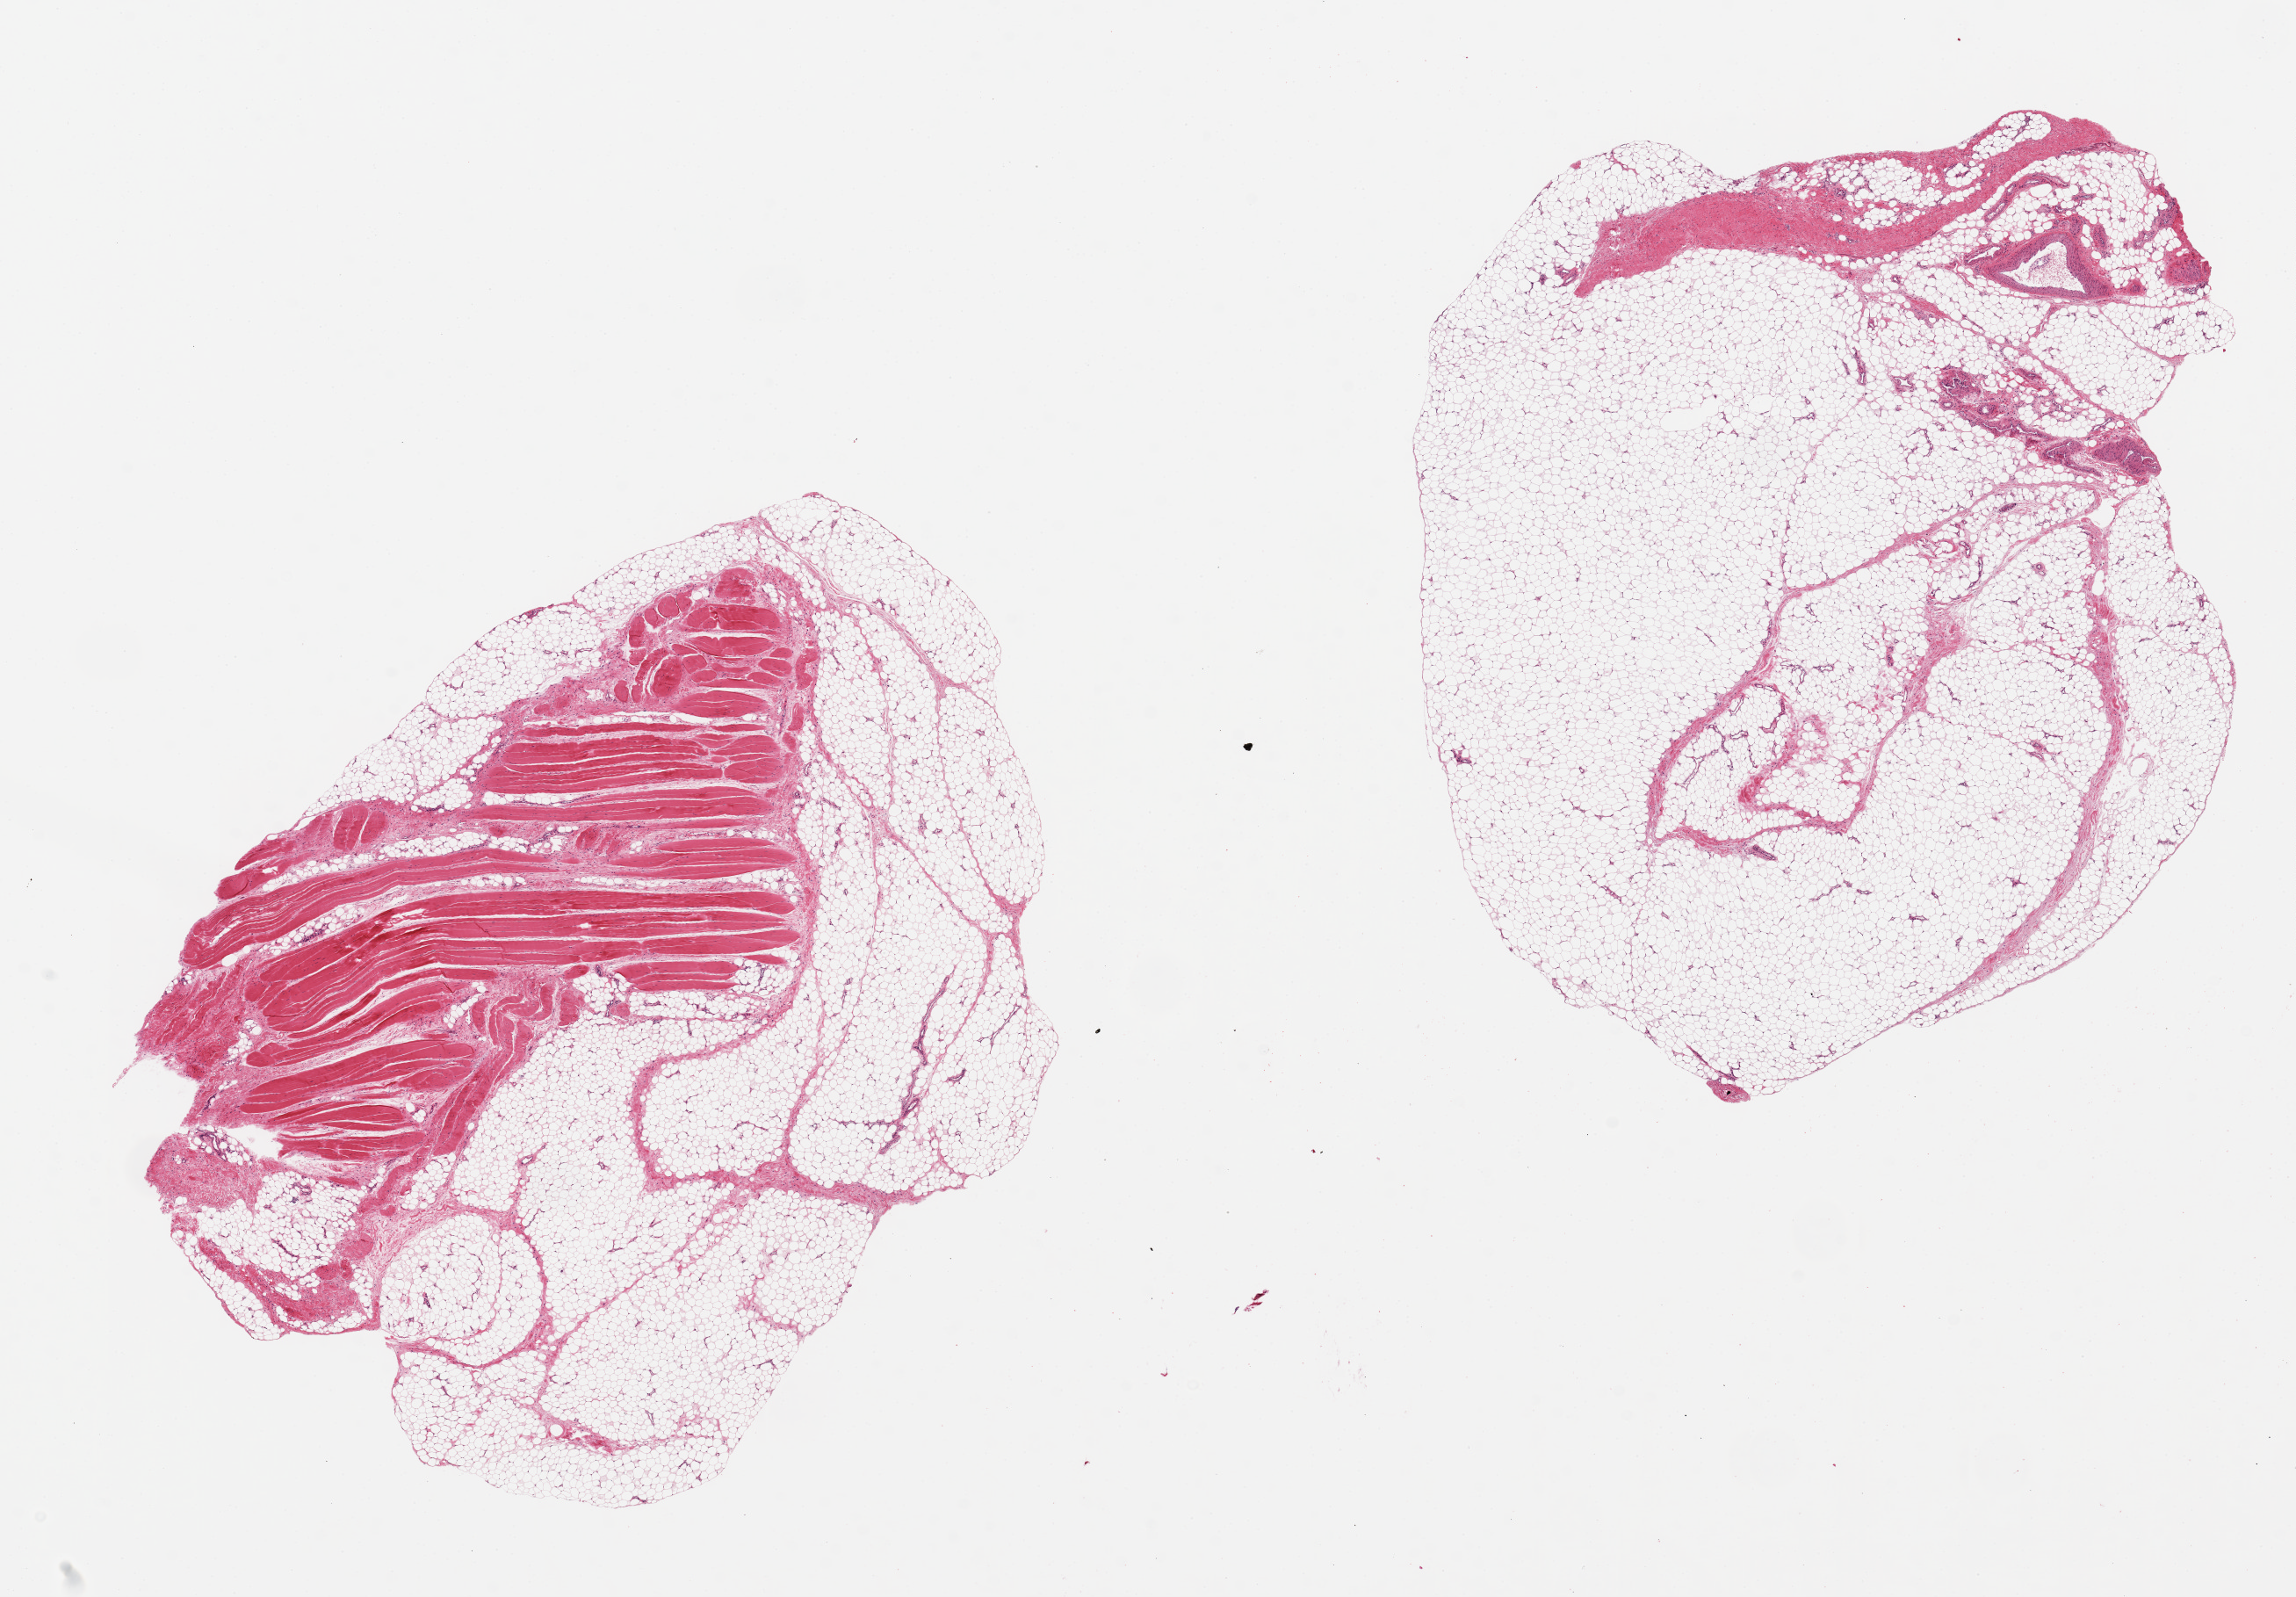
Whole-slide image, H&E stain, brightfield — low-resolution overview of the scanned area, about 20.7 x 14.4 mm (acquisition: 20x scan), PAXgene-fixed paraffin-embedded (PFPE) section, section of adipose tissue (target tissue), donor tissue sample. Male donor.
Pathologist's review note for this sample: 2 pieces, 9x7 & 9x7mm; 1 with 50% fibrous tissue (tendon).